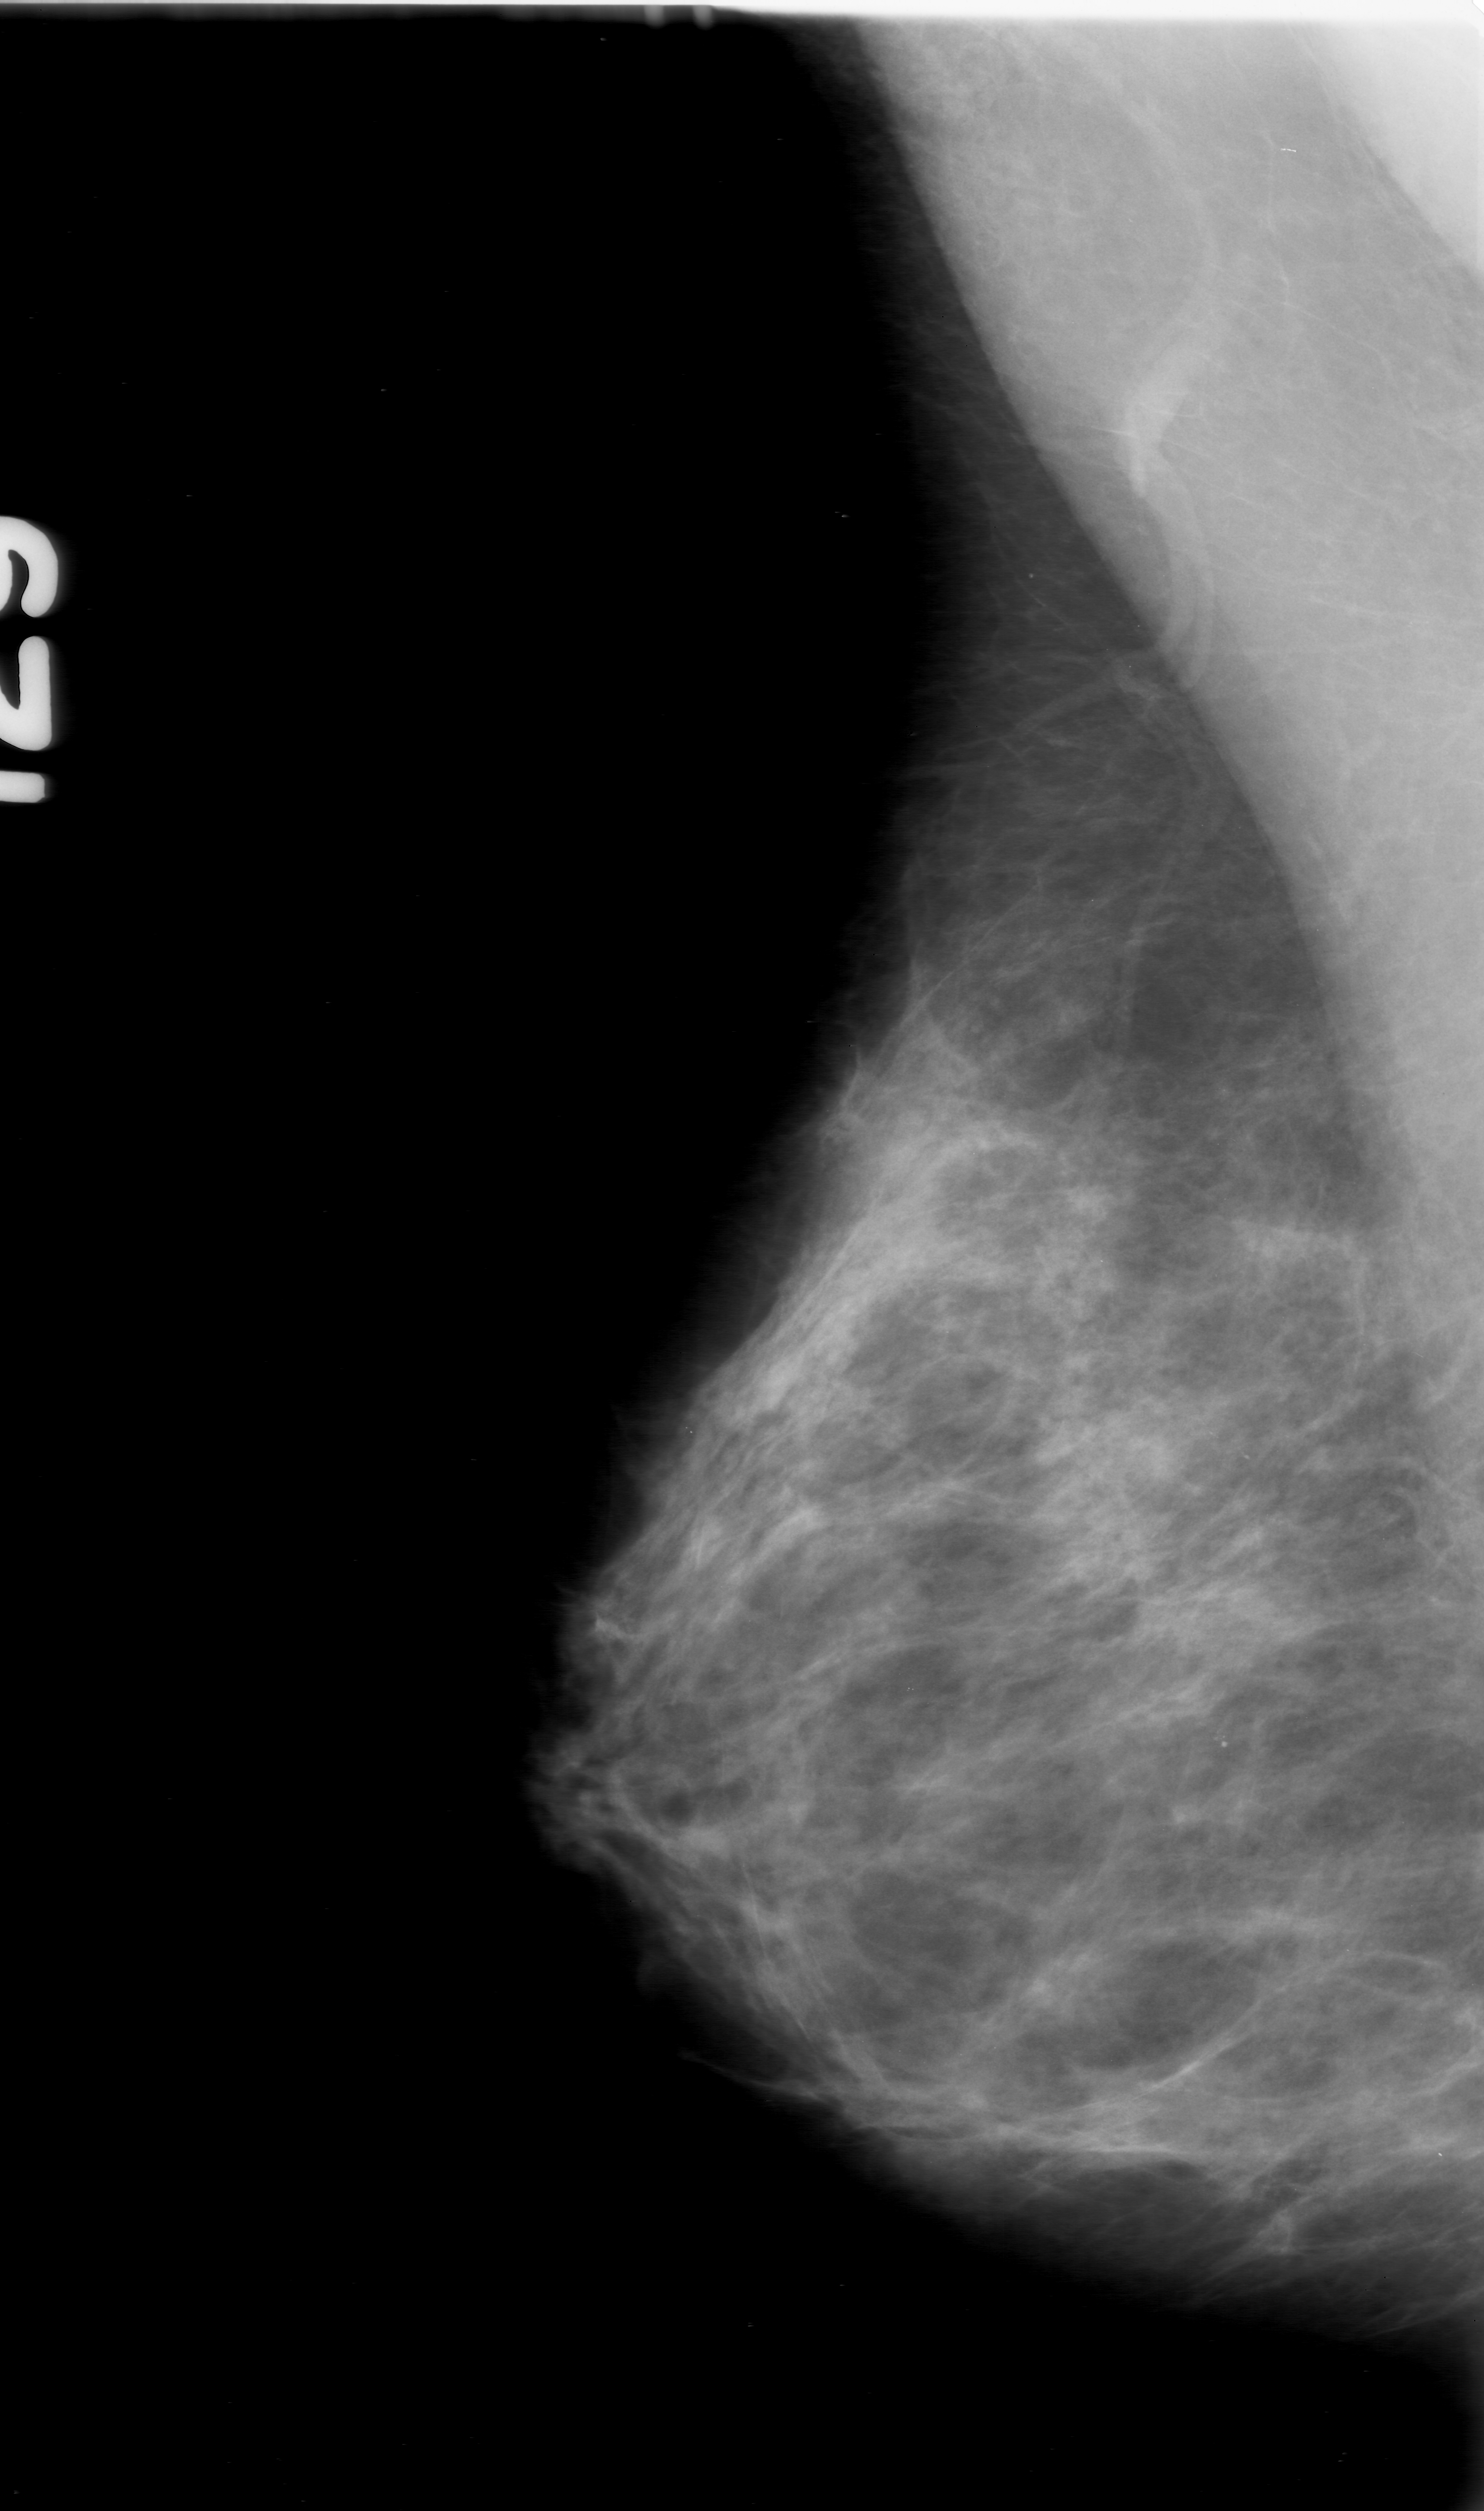
Scanned film-screen mammogram; right breast; MLO view; 1484 × 2511 image matrix.
Expert-marked regions of interest on this image (one box per marked abnormality):
- calcifications, morphology punctate, distribution clustered; BI-RADS assessment category 0; subtlety rating 2 on a 1 (subtle) to 5 (obvious) scale; pathology (as recorded): malignant: bounding box (x1, y1, x2, y2) in pixels: (1128, 1357, 1312, 1535)